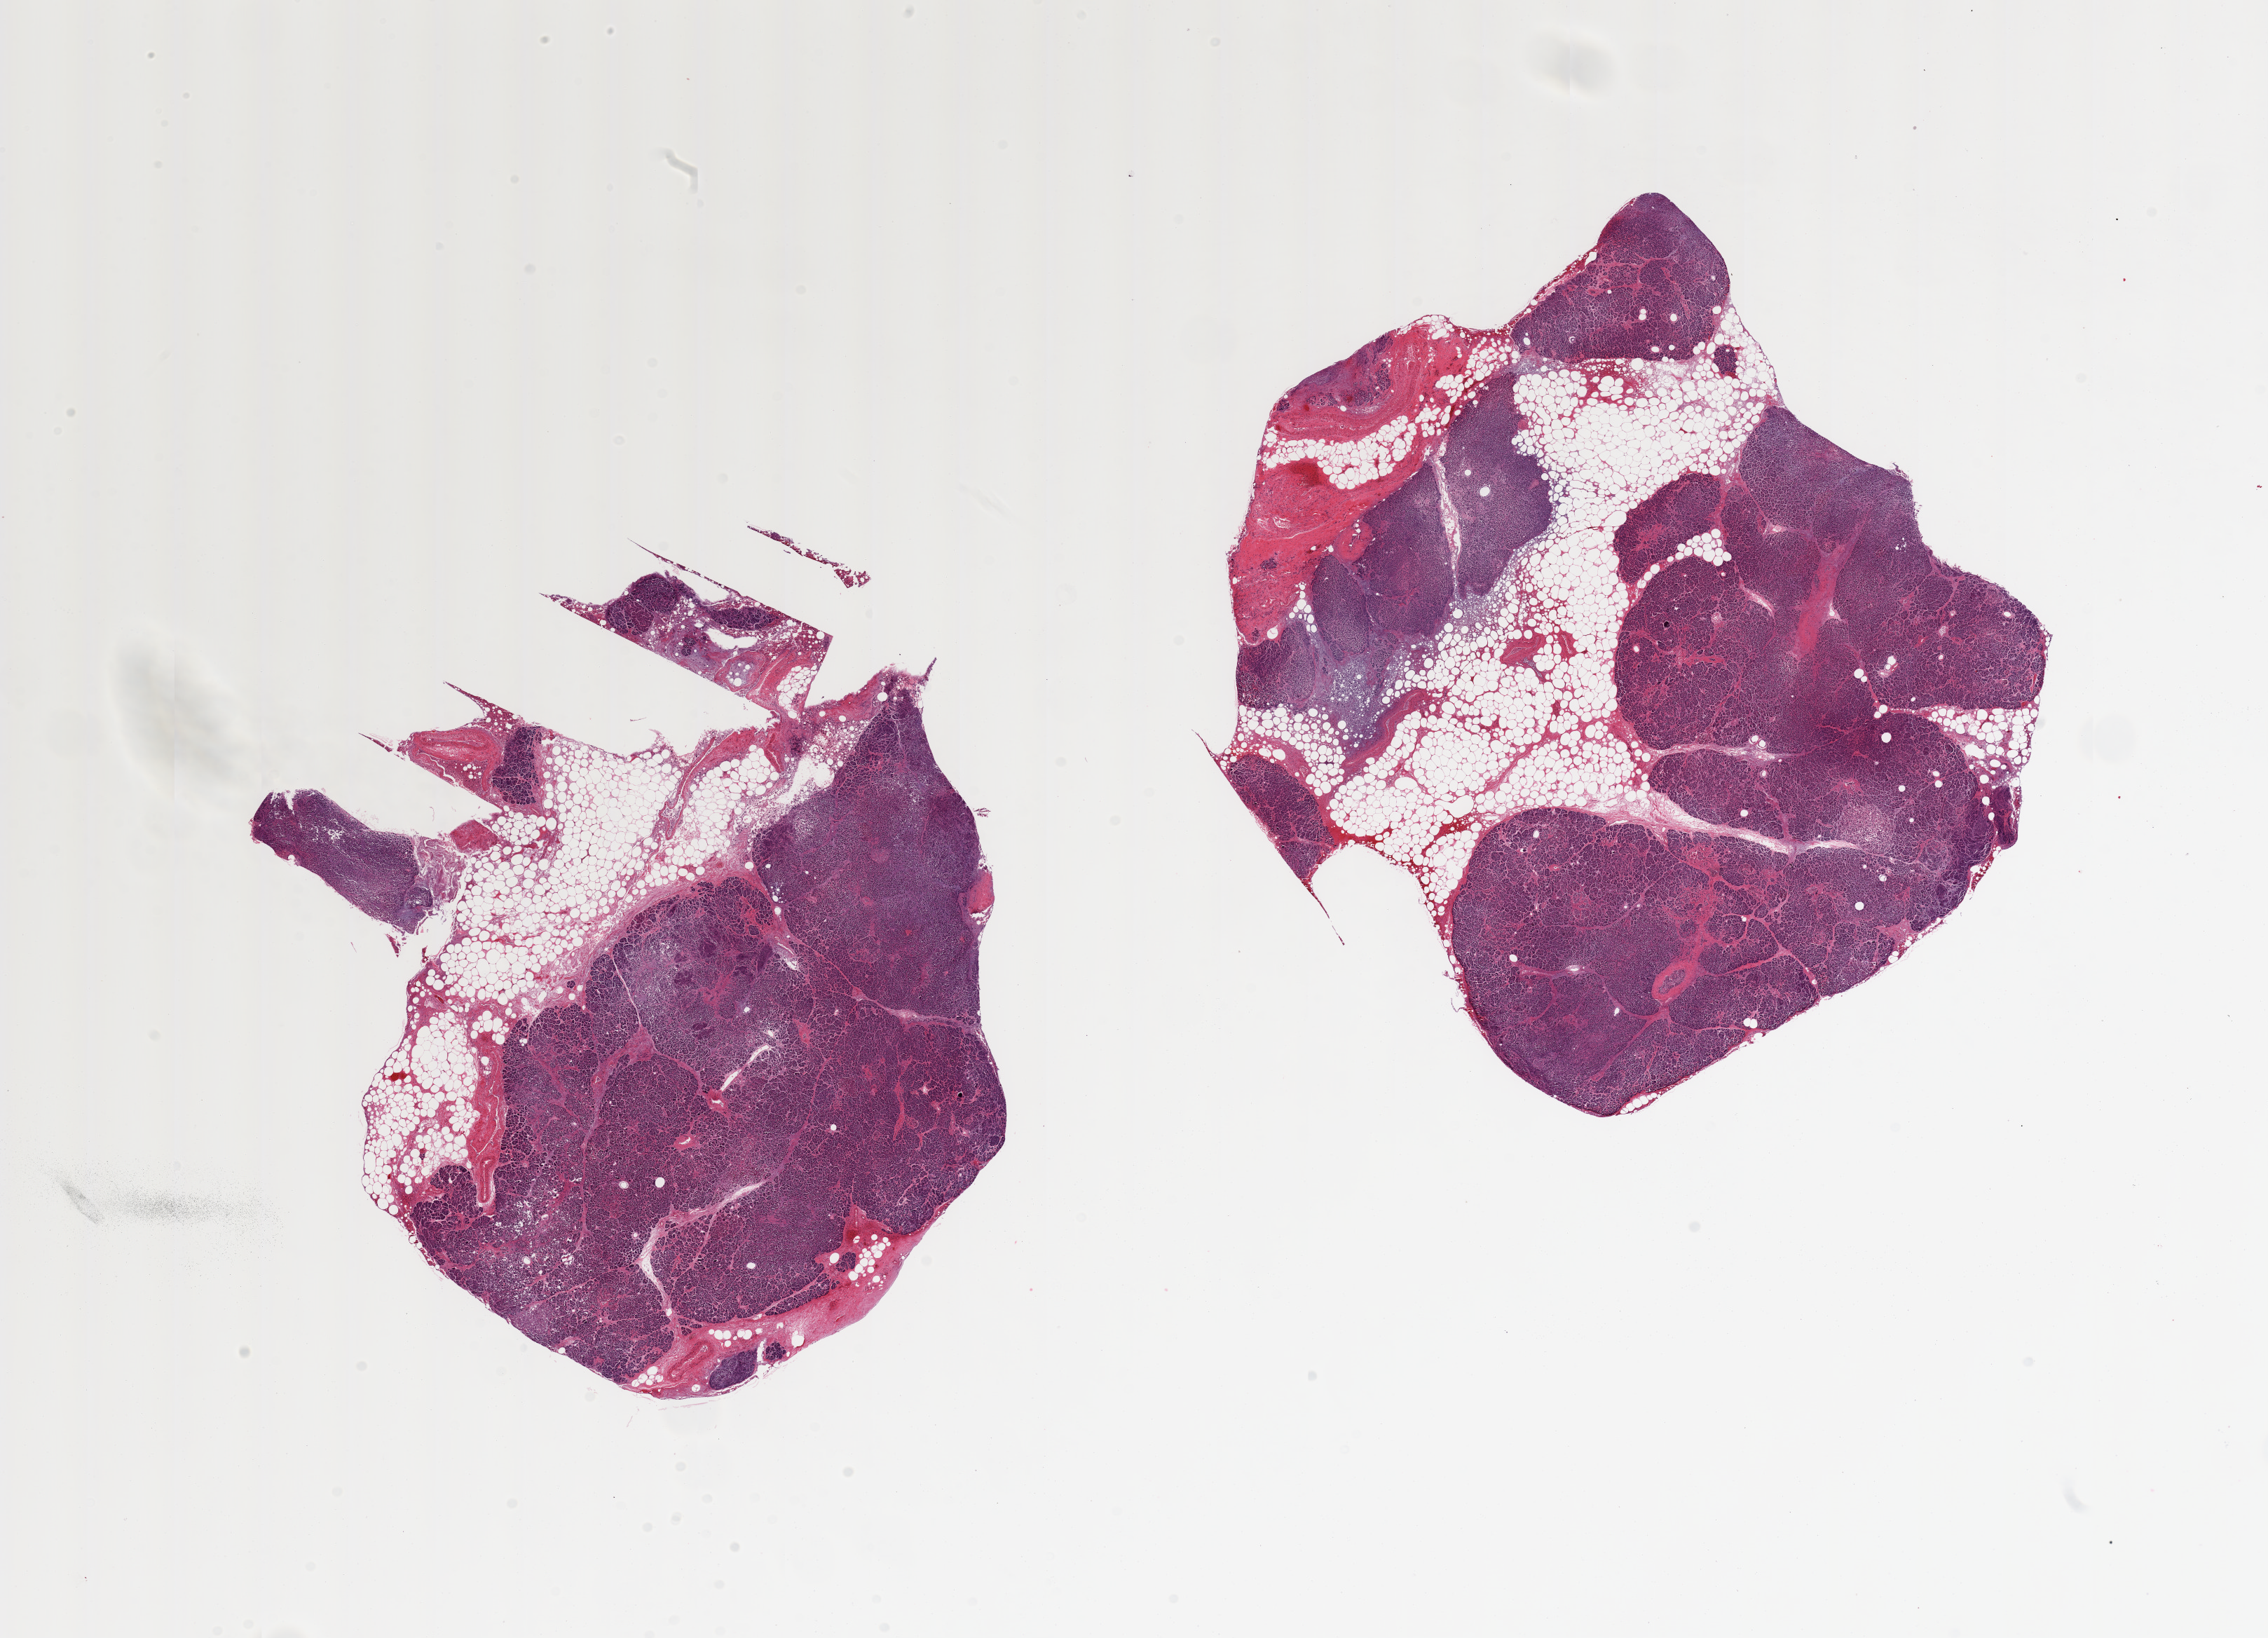
Digitized hematoxylin and eosin (H&E)-stained section, shown as a low-resolution overview of the whole scanned area (about 25.6 x 18.5 mm, from a 20x scan). PAXgene-fixed, paraffin-embedded tissue. Section of pancreas (target tissue). Tissue donor sample. Male donor.
Review note (as recorded): 2 pieces, ~30% is fat, autolysis/saponification.